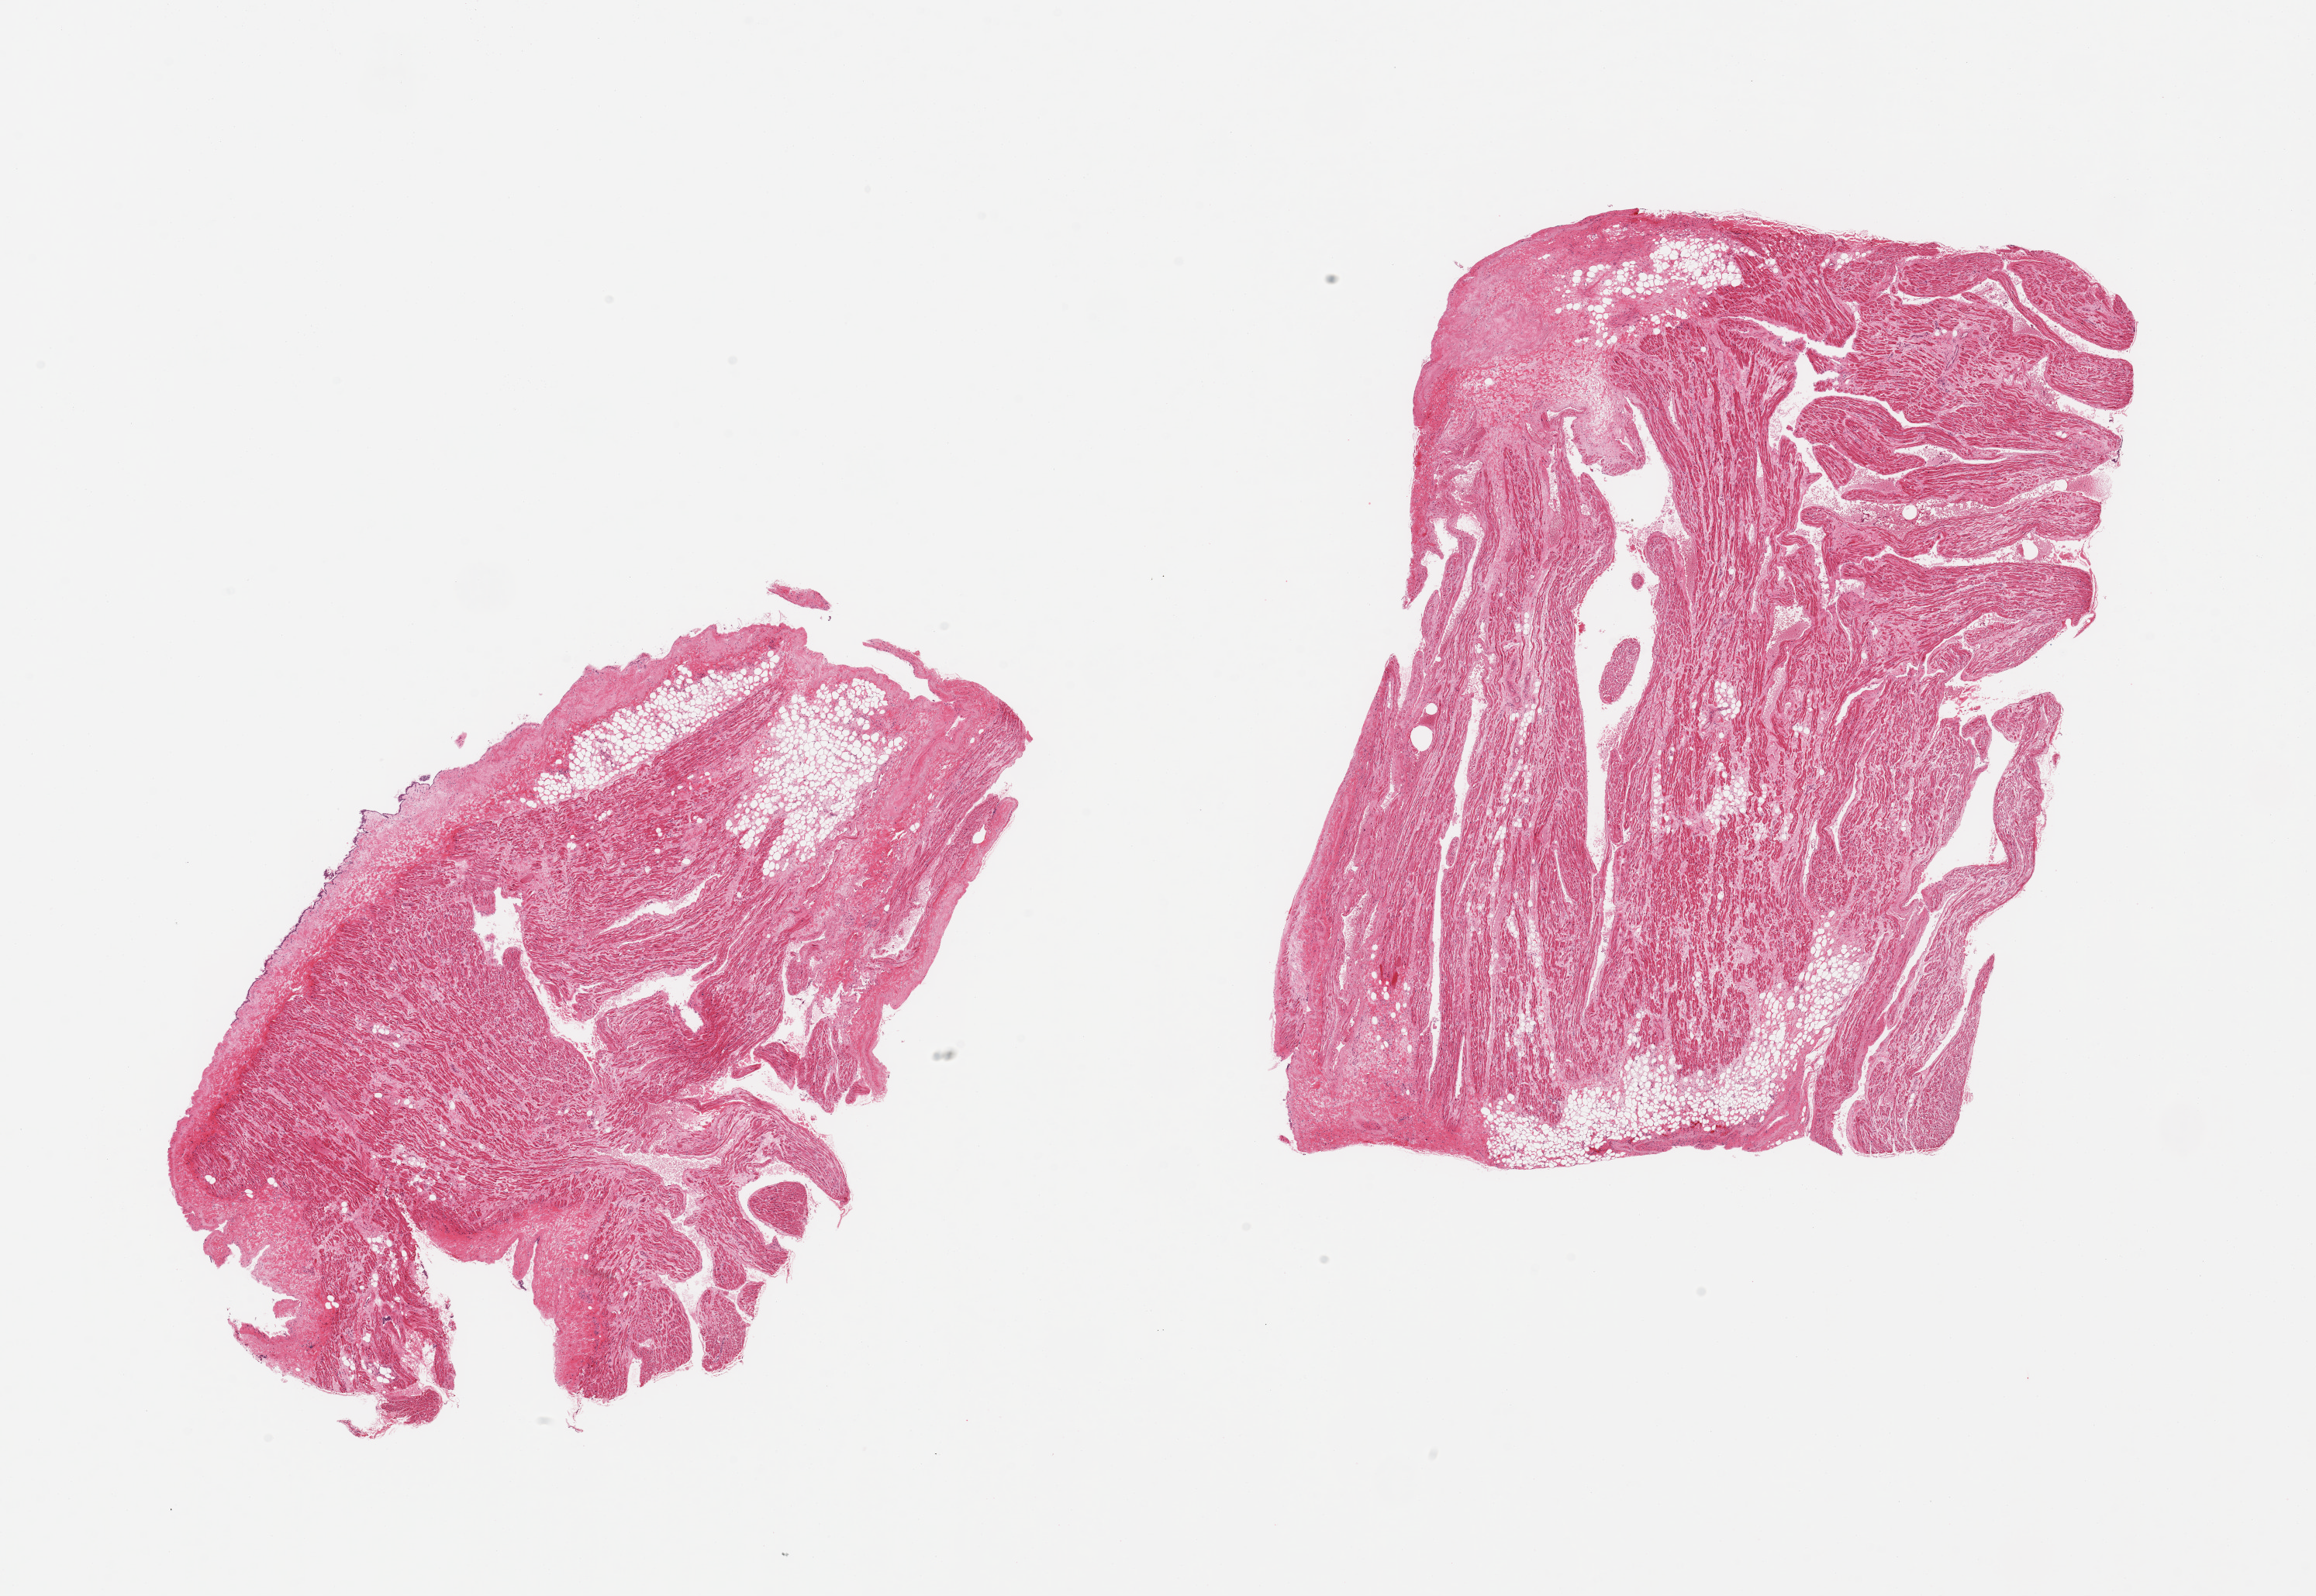
Digitized hematoxylin and eosin (H&E)-stained section — low-resolution overview of the scanned area, about 23.6 x 16.3 mm, PAXgene-fixed paraffin-embedded (PFPE) section, target tissue: auricular appendage, tissue donor sample.
- review note (as recorded): 2 pieces; includes ~10% internal fat